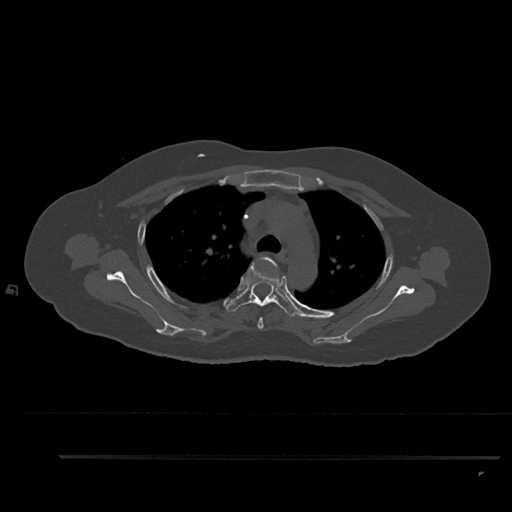
CT including the spine, one axial slice. 120 kVp. Bone window (W 1800 / L 400 HU). 0.5 mm slice thickness. 512 × 512 image matrix, field of view 408 × 408 mm. Patient: female, 44 years. Case-level facts recorded for this patient, not image findings: primary cancer: renal; vertebrae with lytic lesions (as recorded): L1.
Outlined on this slice (semi-automatic segmentation, software-assisted and operator-edited):
- T3 vertebra: bounding box <252,256,279,329> (left, top, right, bottom; pixels)
- T4 vertebra: <226,265,298,317>